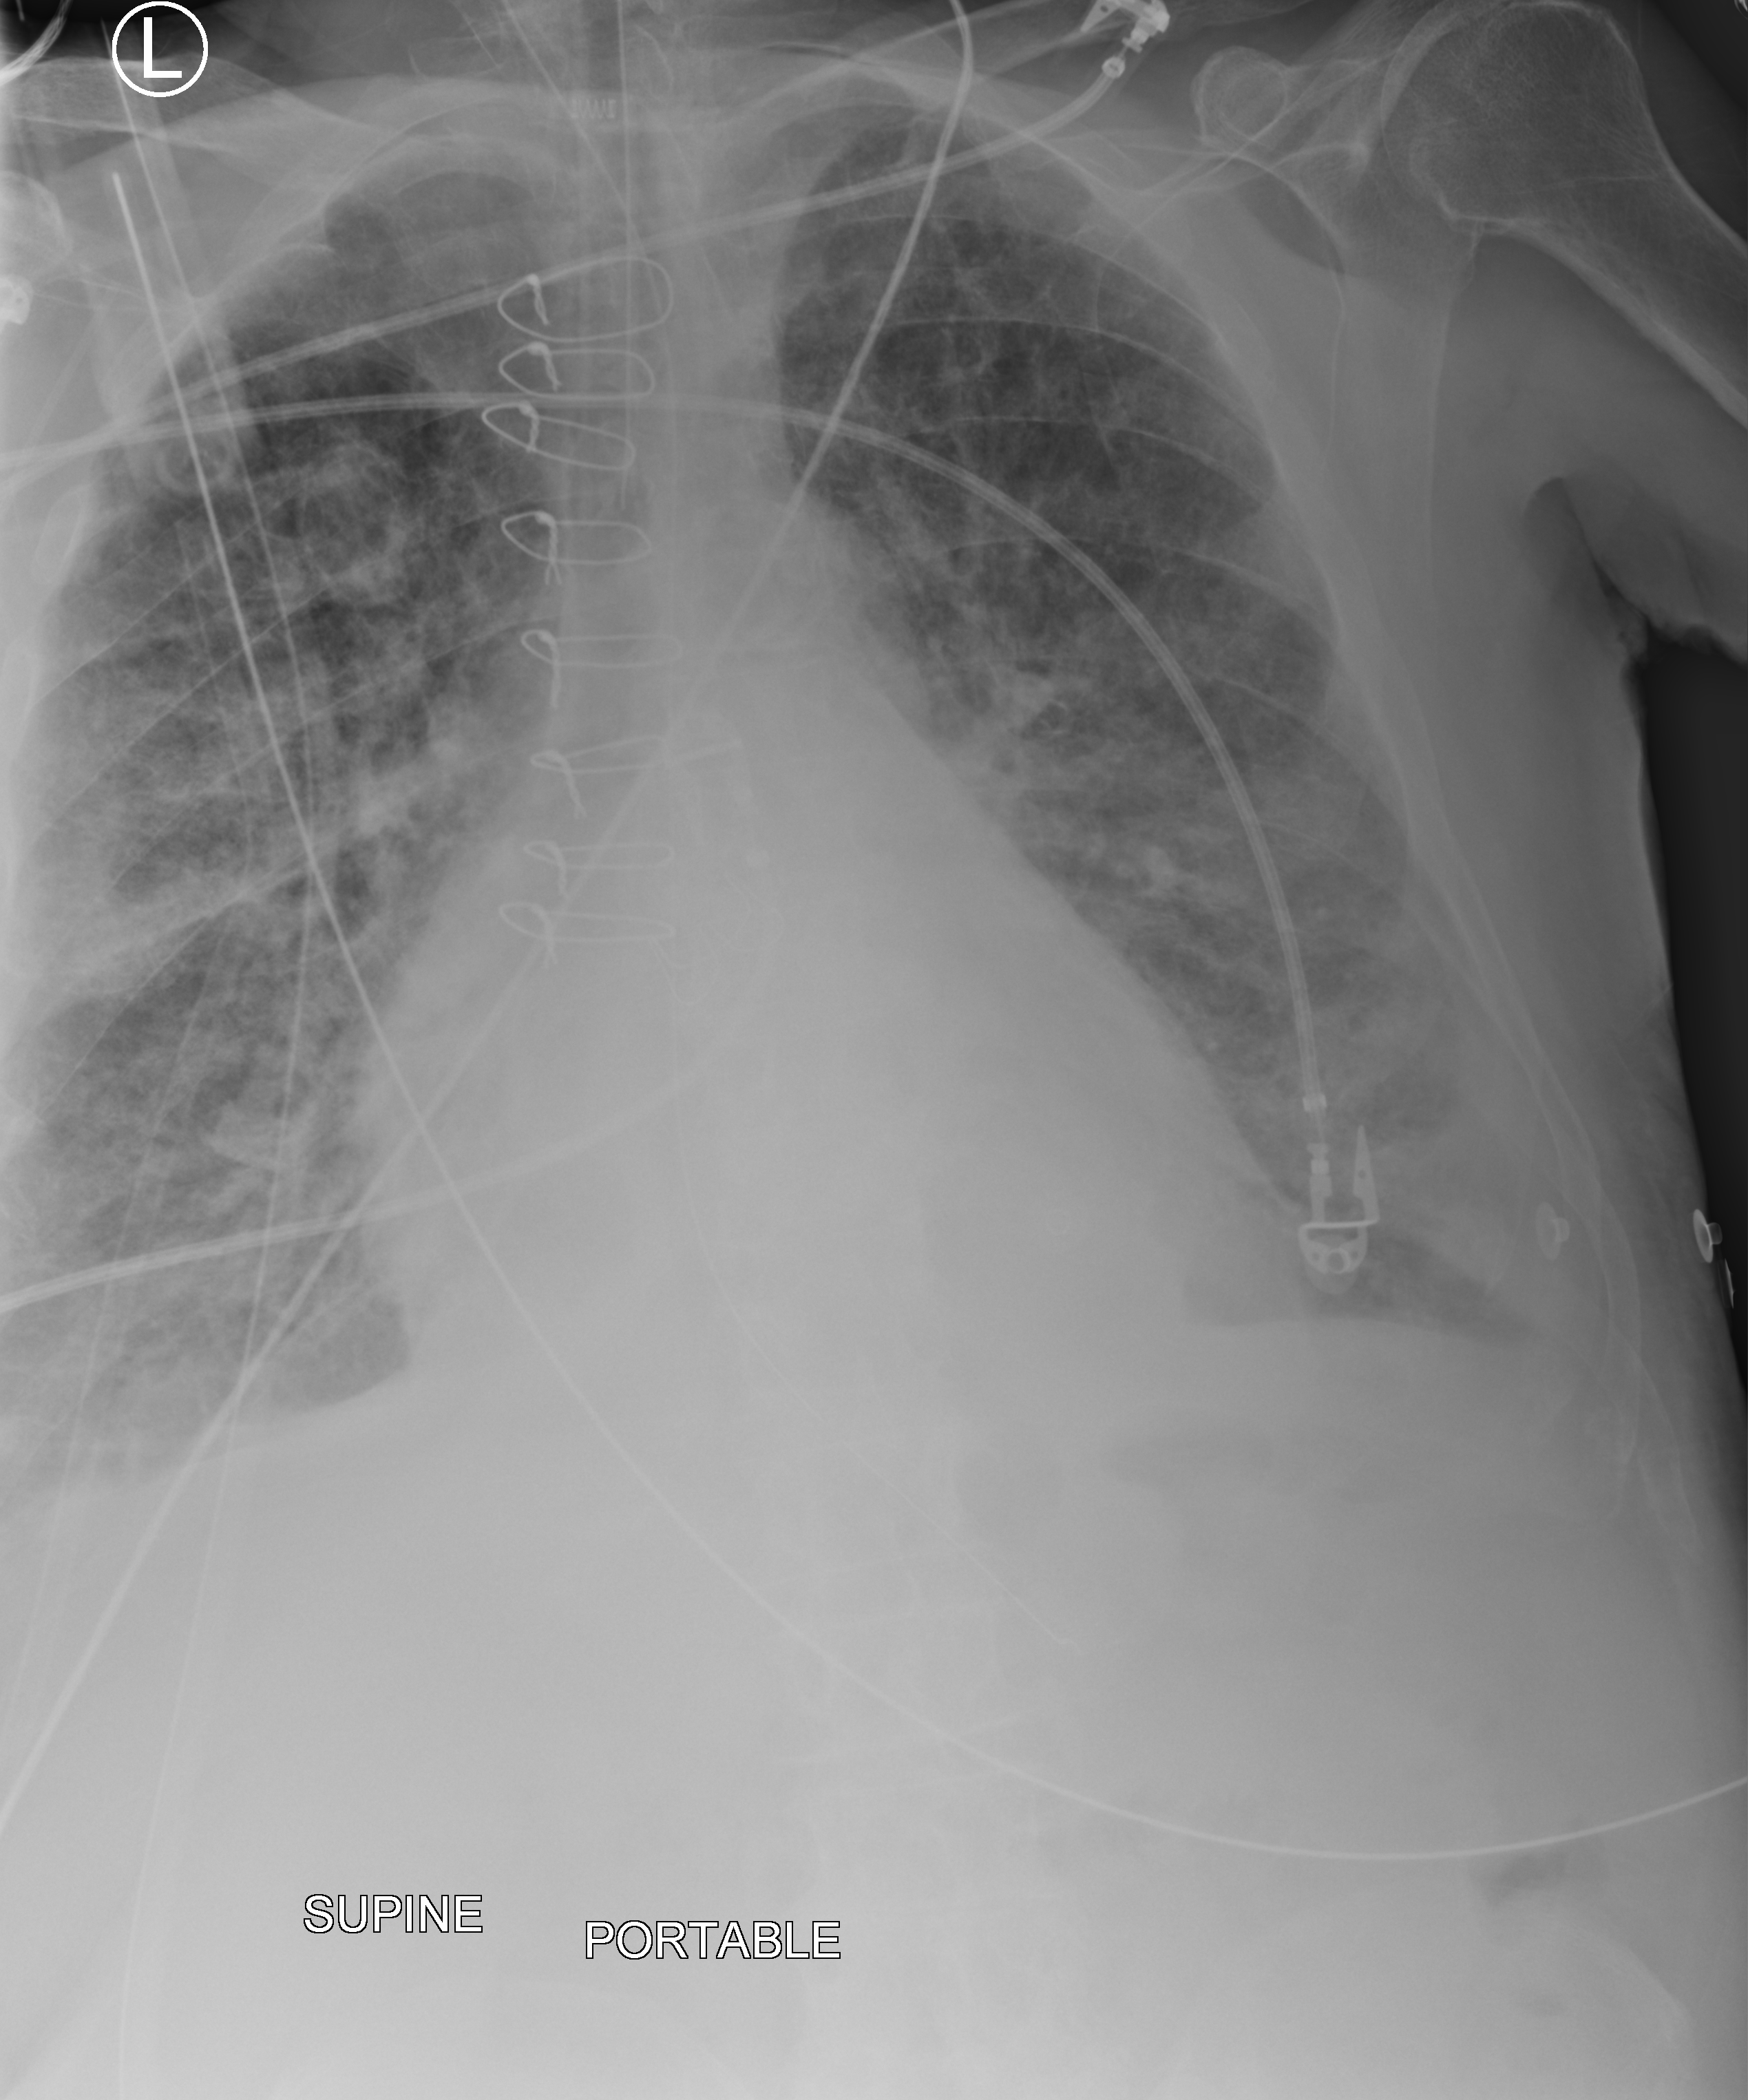
Chest radiograph (computed radiography); anteroposterior (AP) projection. Patient hospitalised with COVID-19; male, aged 75–90 years.
Hospital-stay facts (about this admission, not read from this image; timing relative to this image not recorded): mechanically ventilated during this hospital stay: yes; admitted to intensive care during this hospital stay: yes.